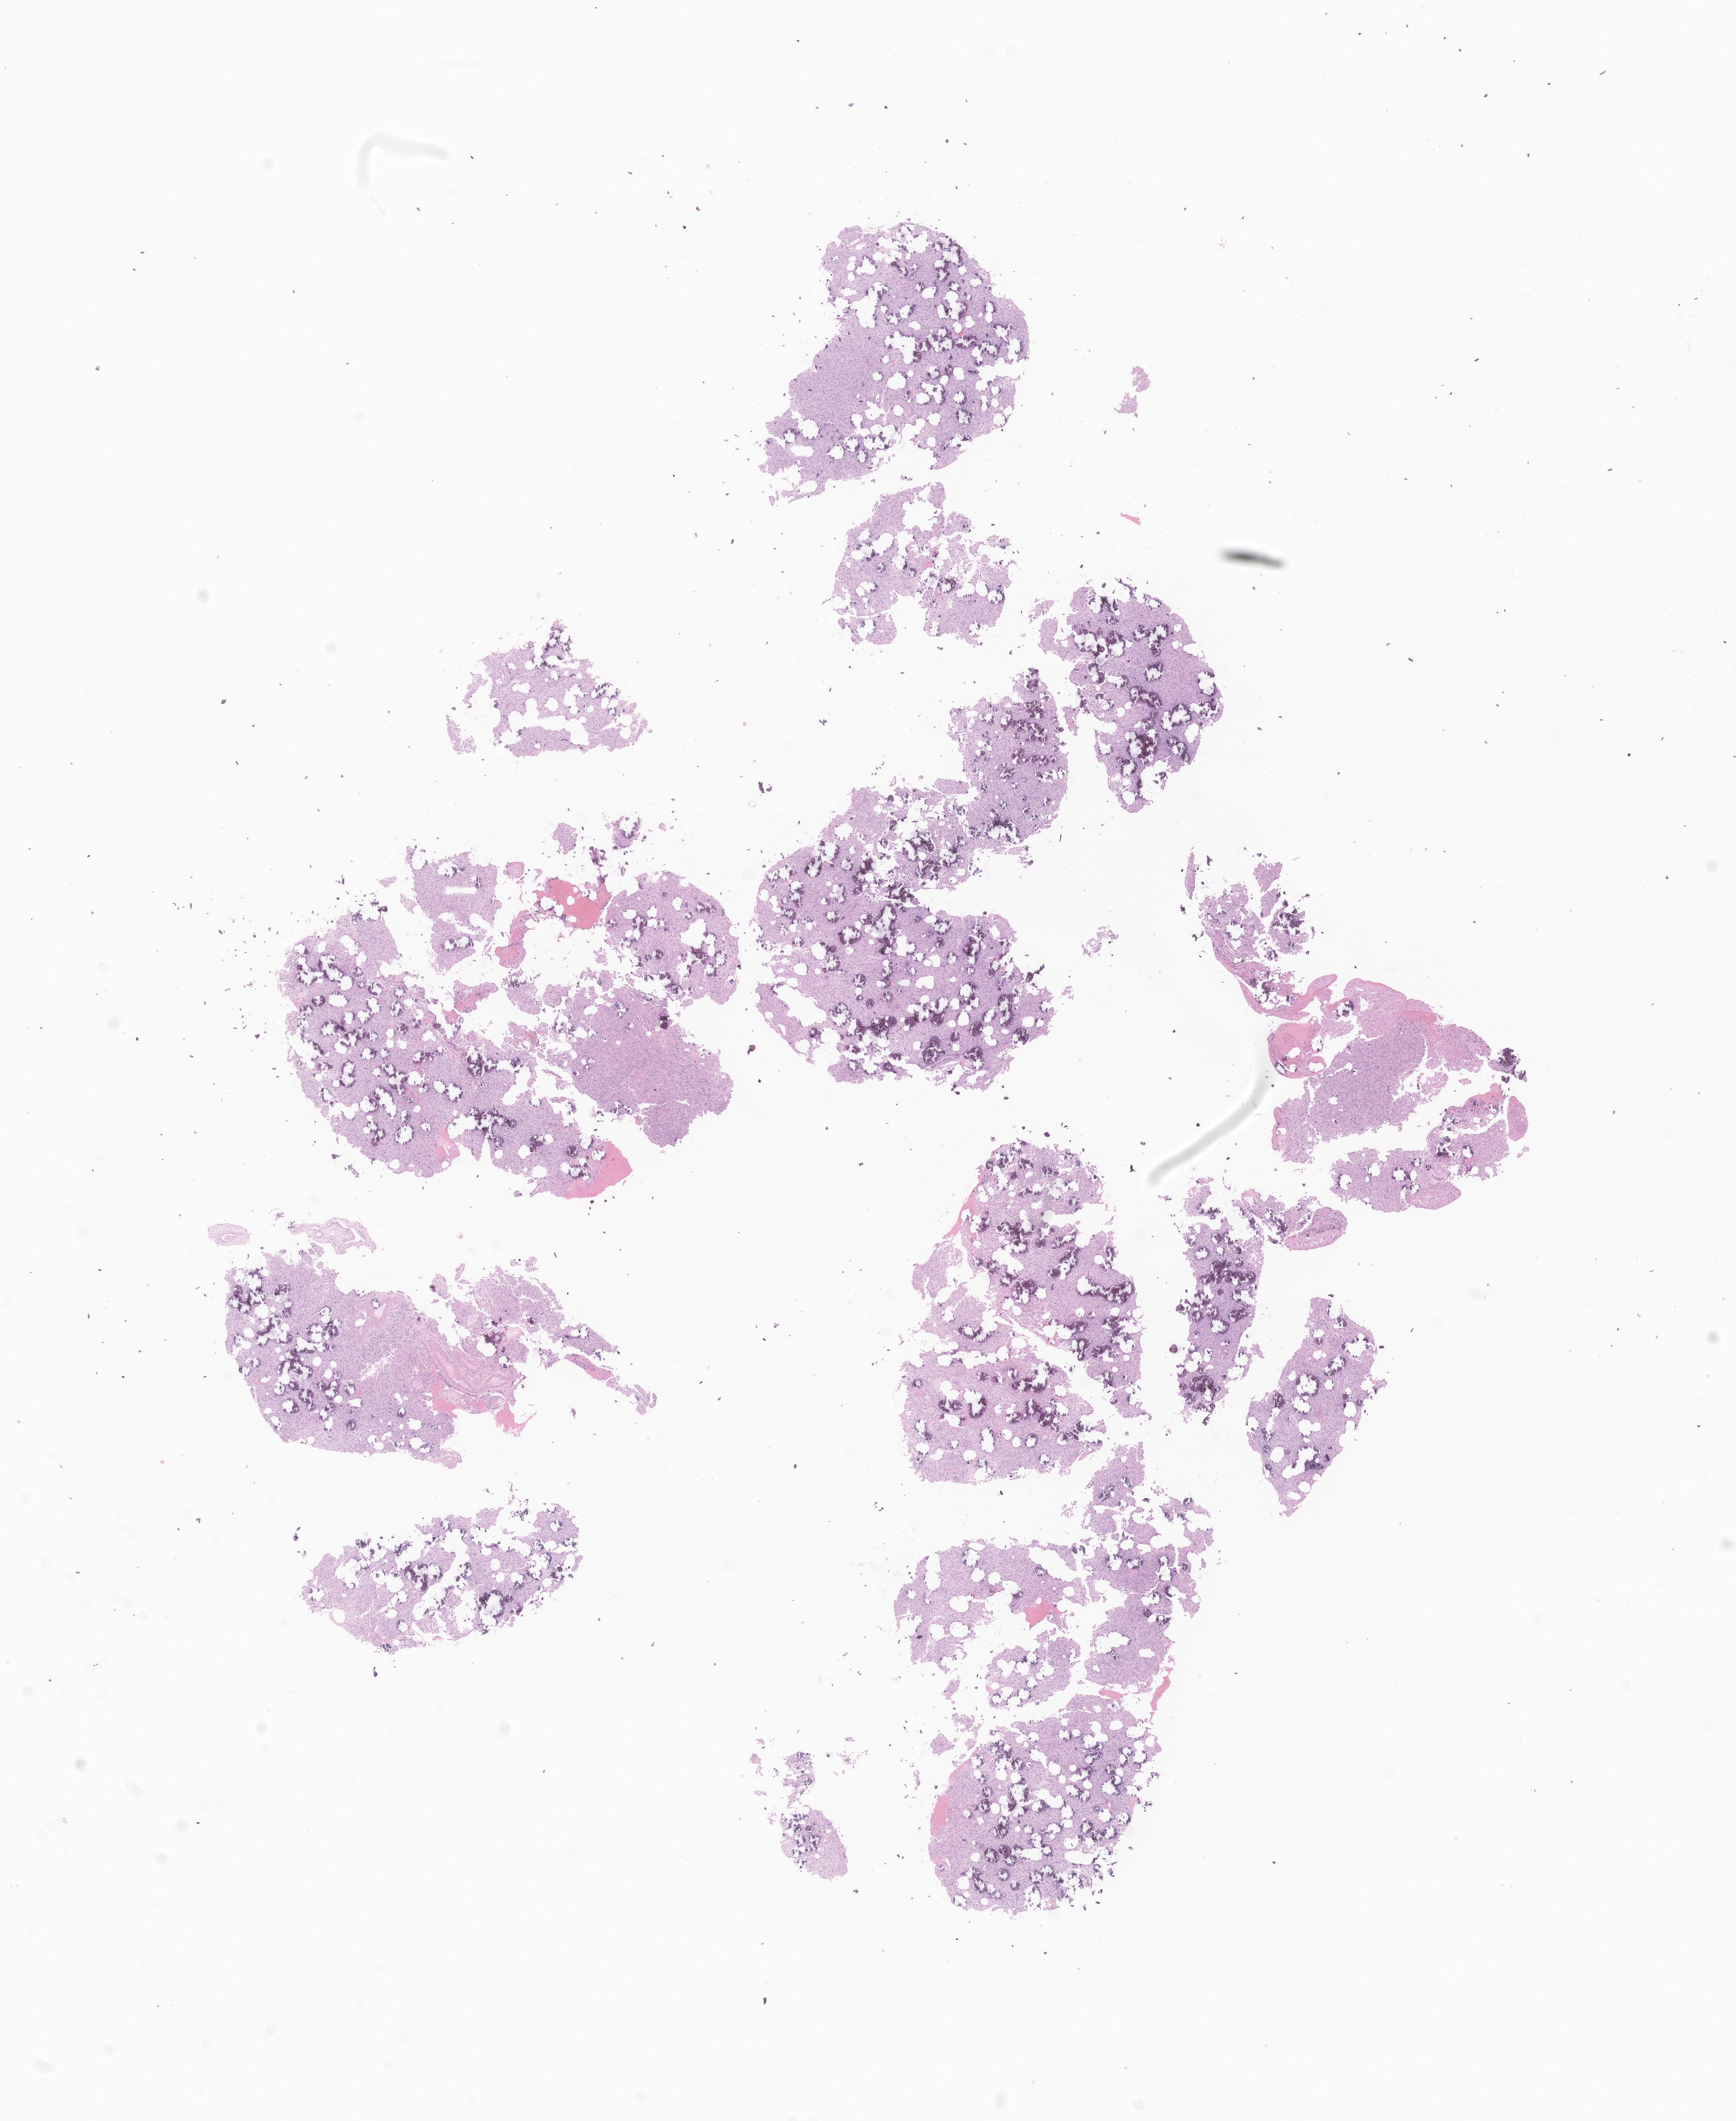
Digitized H&E-stained section of tumor tissue from the brain, low-resolution overview of the scanned area, about 15.5 x 18.9 mm, formalin-fixed, paraffin-embedded (FFPE) tissue. Female patient, age 58 months (4 years 10 months).
Diagnosis (ICD-O-3 morphology term): Neoplasm, malignant.